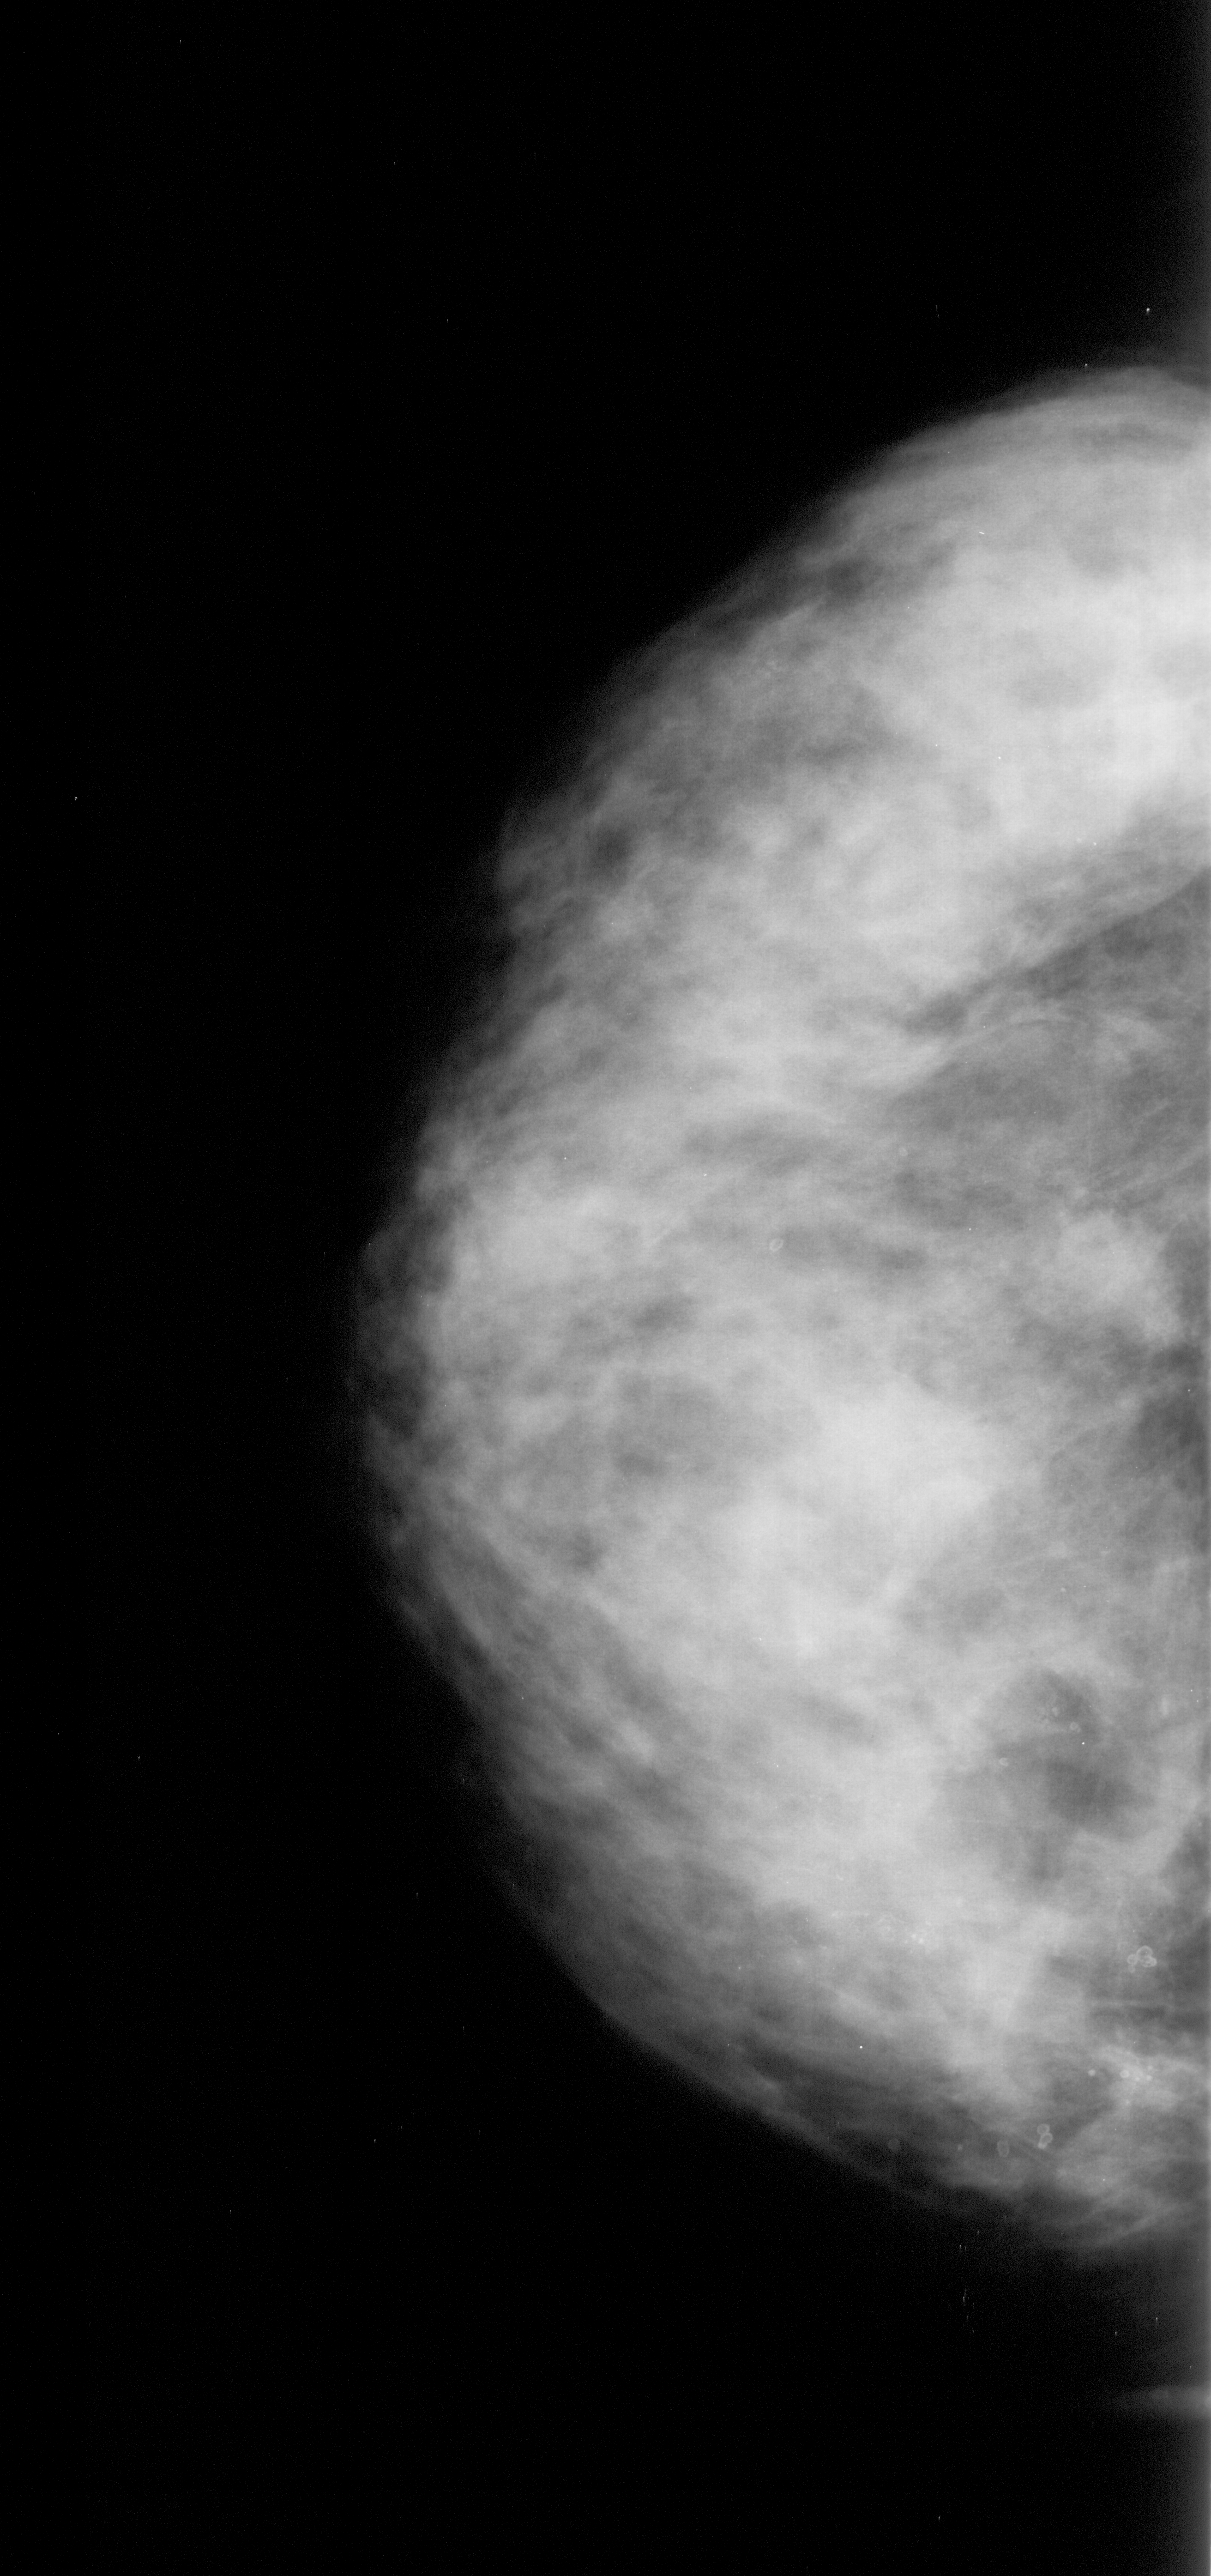
Digitized screen-film mammogram; left breast; CC view; BI-RADS breast density category 3 (scale 1–4).
- Finding: calcifications, morphology pleomorphic, distribution clustered; BI-RADS assessment category 4; subtlety rating 2 on a 1 (subtle) to 5 (obvious) scale; pathology (as recorded): malignant.